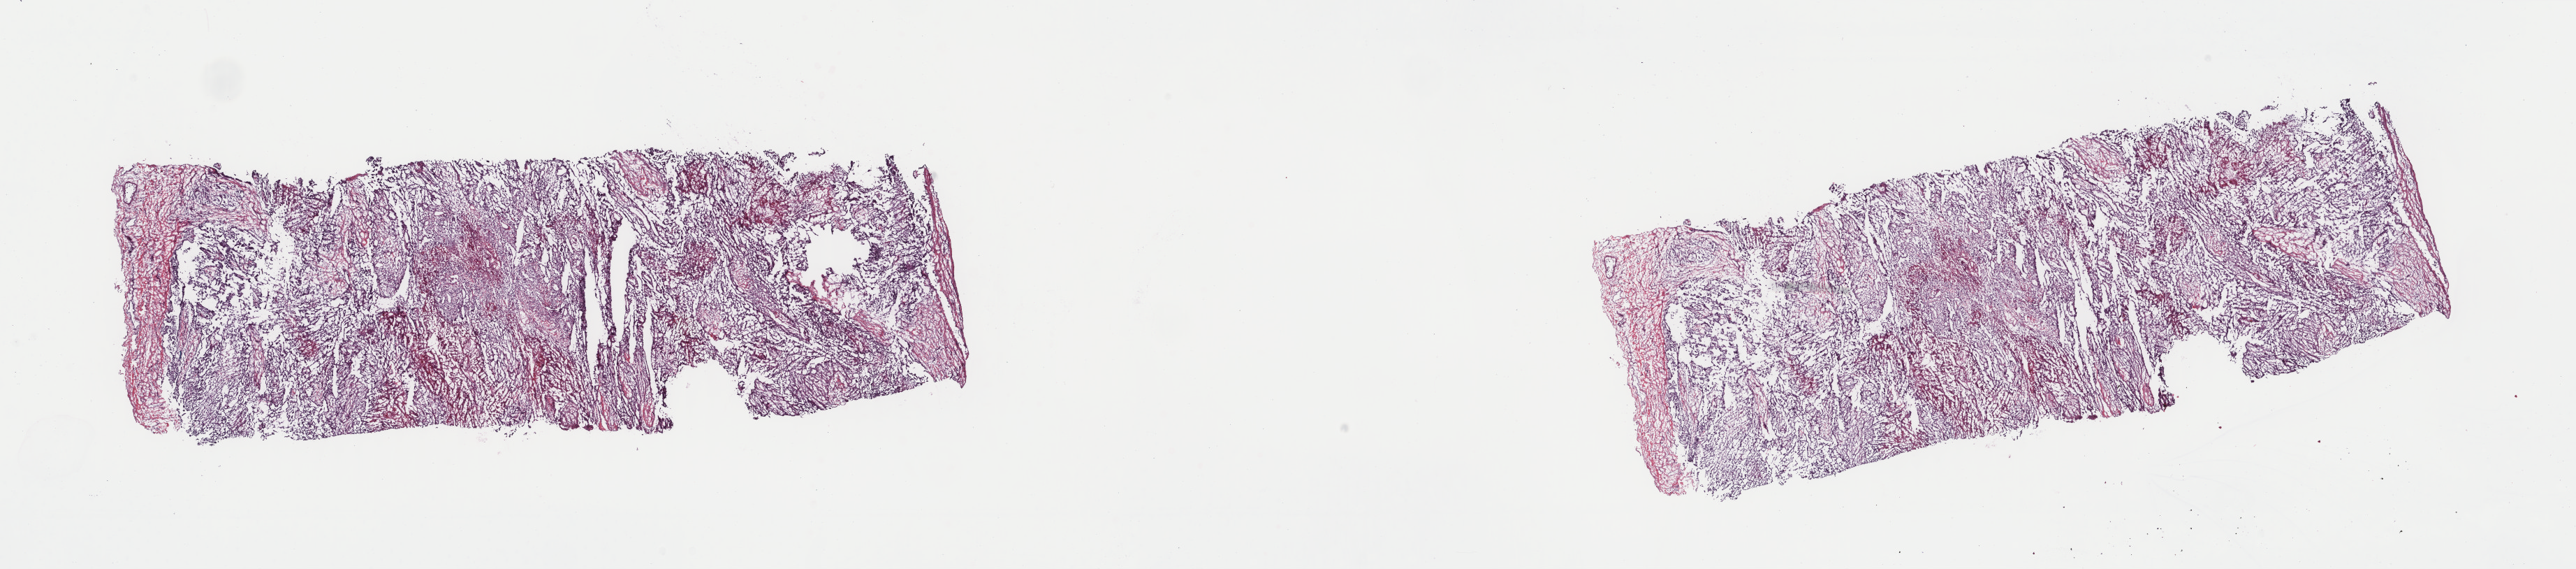
Whole-slide histology image, H&E-stained — a low-resolution overview of the entire scanned area, about 29.3 x 6.5 mm (from a 40x scan). Frozen section. Primary tumour sample from the mesothelium. Patient: male, age at initial diagnosis 67 years. Slide review estimates, as recorded: tumour cells 100%, tumour nuclei 80%, normal cells 0%, stromal cells 0%, necrosis 0%. Inflammatory infiltration, as recorded: lymphocyte infiltration 2%, monocyte infiltration 0%, neutrophil infiltration 0%.
TNM: T3 N0 M0. Diagnosis: Mesothelioma, biphasic, malignant (pleura, NOS). Laterality: right. AJCC pathologic stage: III (5th edition).